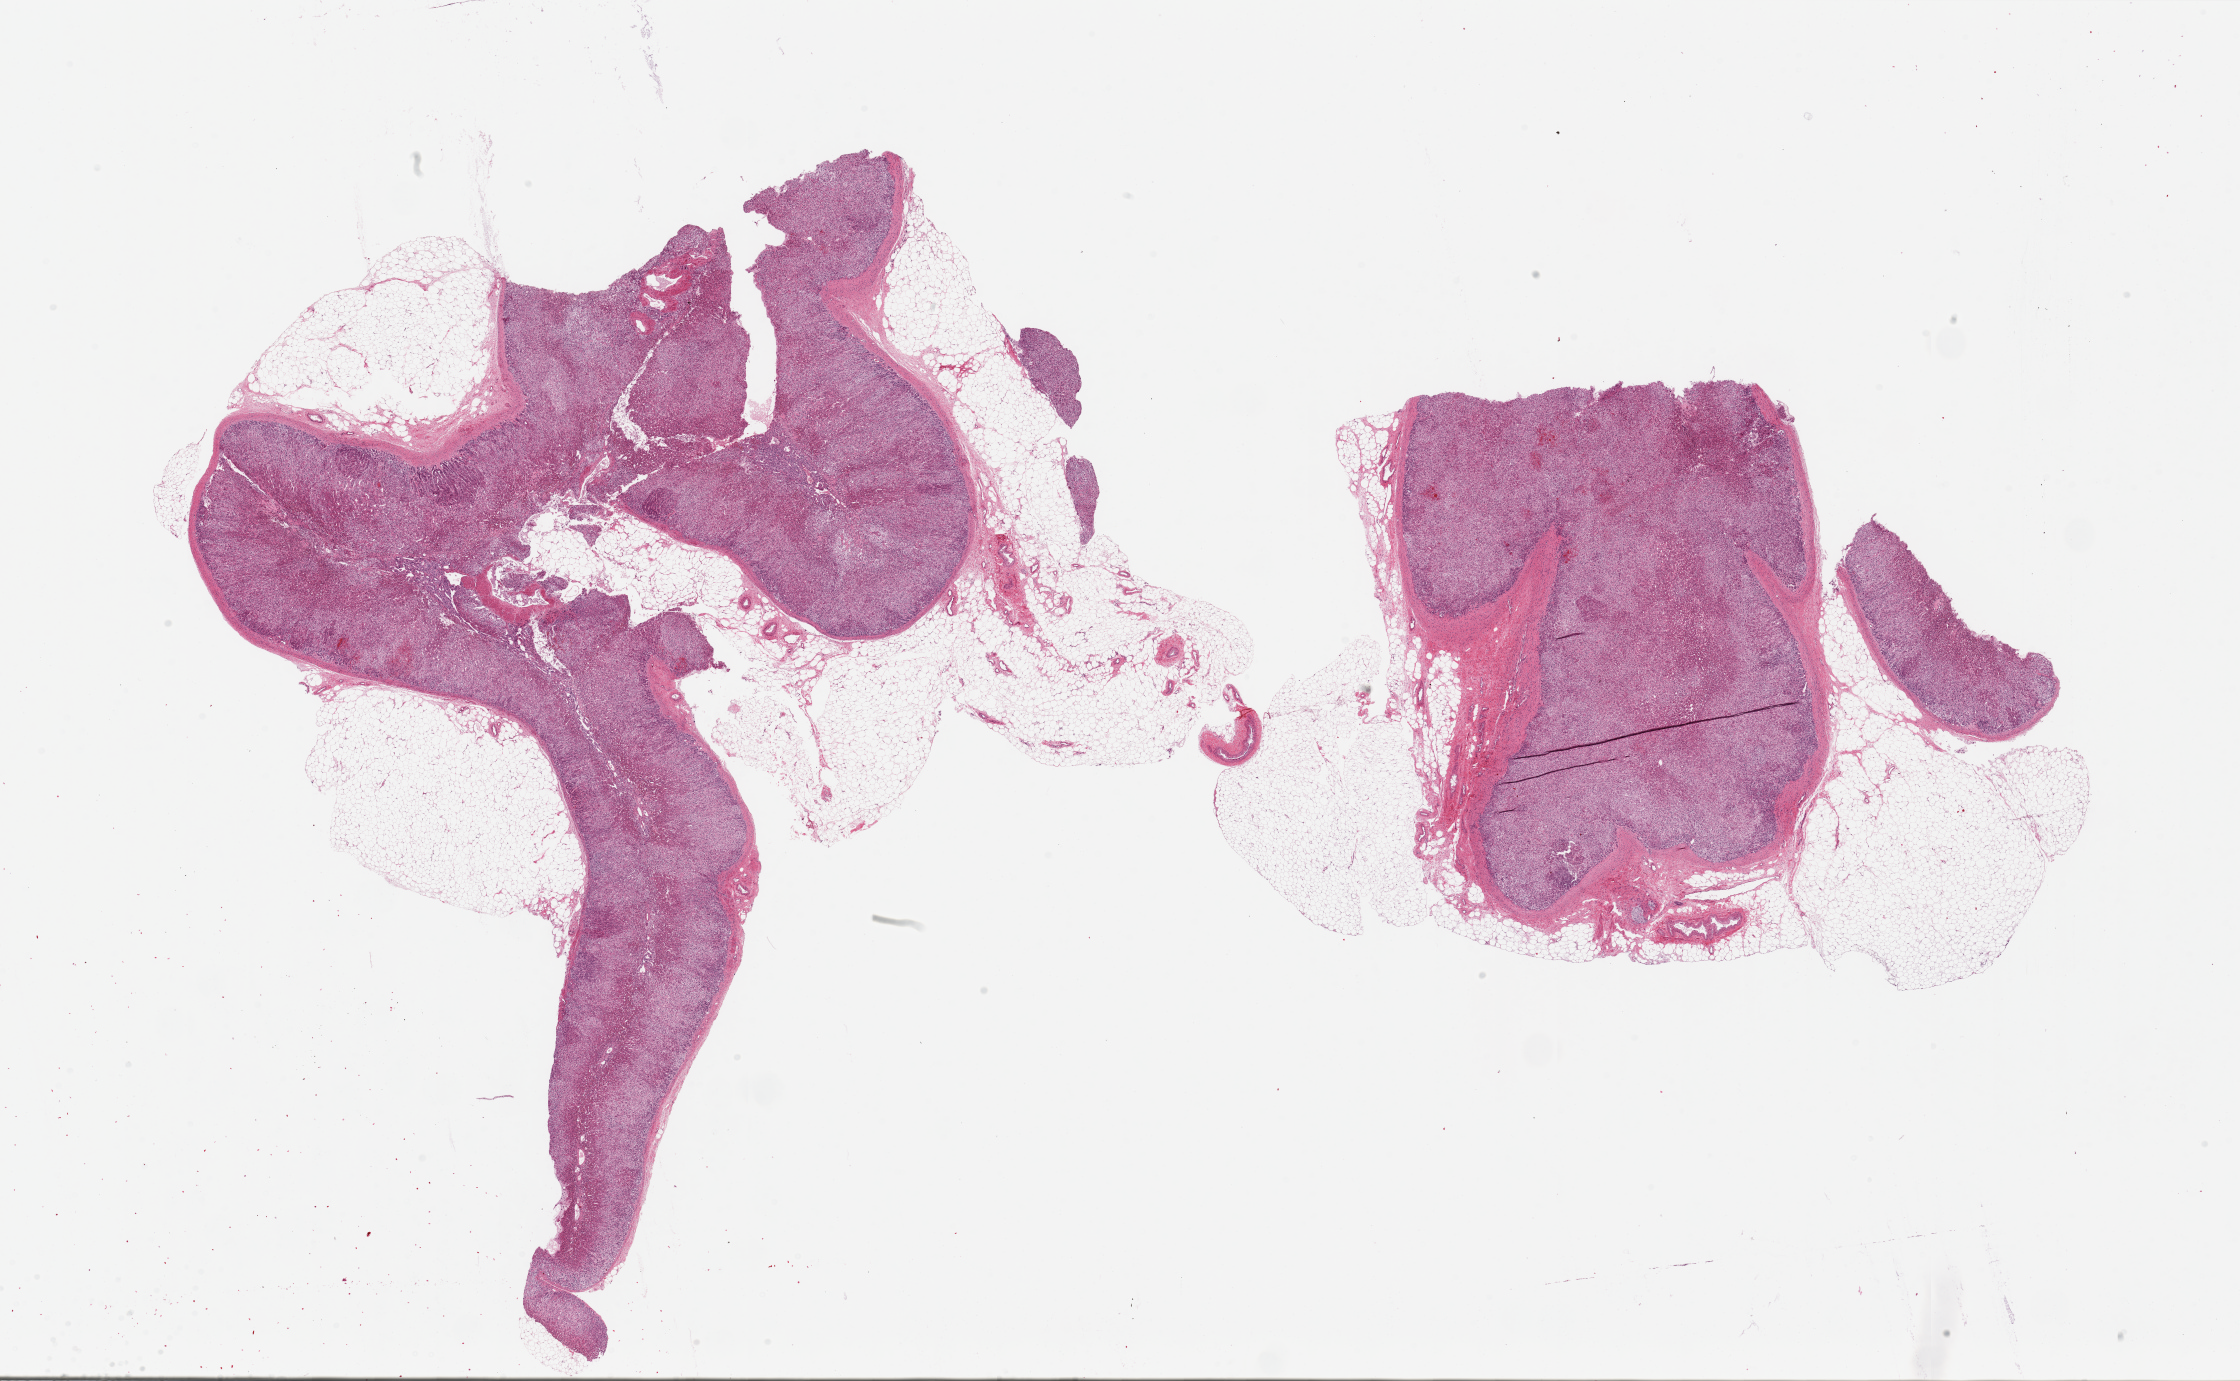
Hematoxylin and eosin (H&E) whole-slide image, a low-resolution overview of the entire scanned area, about 35.4 x 21.8 mm, PAXgene-fixed, paraffin-embedded tissue, section of adrenal gland (target tissue), donor tissue sample.
- pathologist's review note for this sample: 2 pieces, 19x18 & 14x10mm; 40% external adipose. Several capillaries contain fibrin thrombi